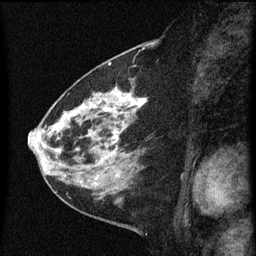
Breast MRI (dynamic contrast-enhanced), one sagittal slice; slice 27 of 60 in the series (ordered by position); dynamic contrast-enhanced series, image 2 of 3 at this slice position (ordered by acquisition); 1.5 T; TE 4.2 ms, TR 8 ms; 2 mm slice thickness; 256 × 256 image matrix, field of view 180 × 180 mm. Female patient, age 60 years.
Outlined on this slice (semi-automatically segmented with operator editing):
- analysis volume of interest (the breast-tissue region the enhancement analysis was run in; not a lesion): bounding box [x1, y1, x2, y2] px = [48, 82, 151, 183]
- tumour enhancement mask (voxels above the 70 % enhancement threshold inside the analysis volume of interest): [52, 92, 146, 161]